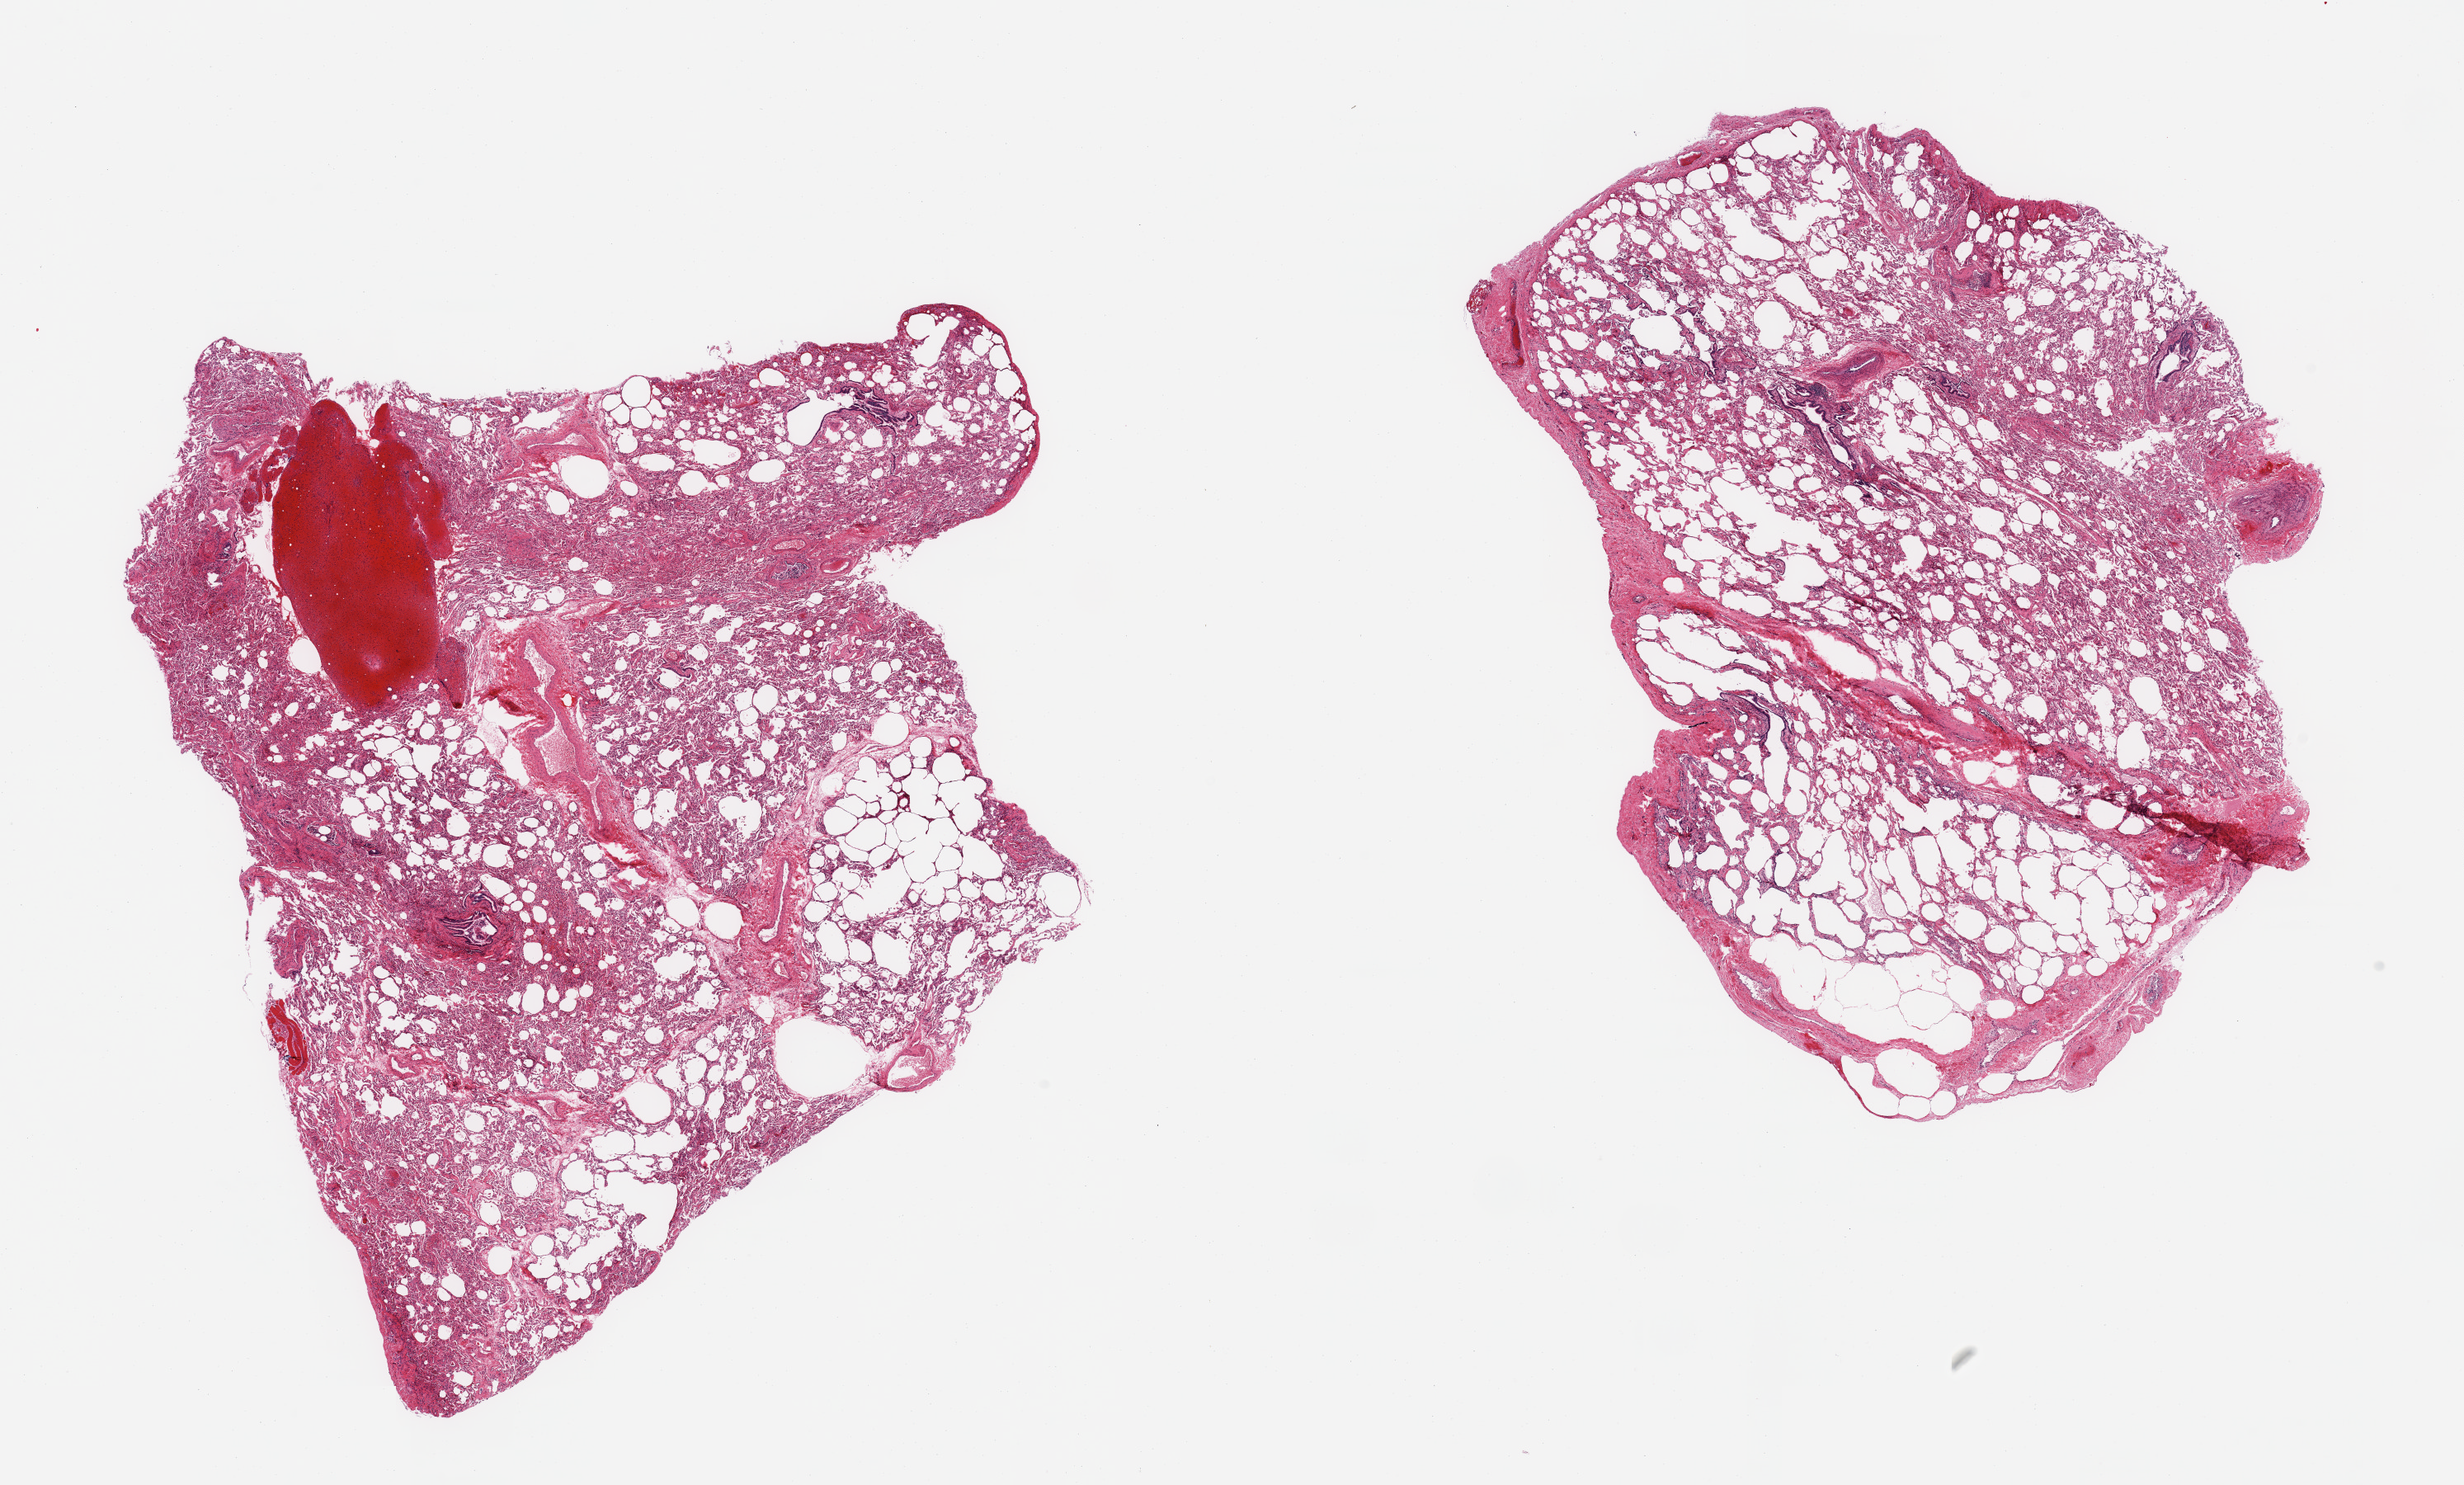
Whole-slide image, haematoxylin and eosin stain, low-resolution overview of the scanned area, about 23.6 x 14.2 mm; PAXgene-fixed paraffin-embedded (PFPE) section; section of lung (target tissue); tissue donor sample. Donor: female.
• reviewer comment on this tissue sample: 2 pieces, mild, focal edema, ataletctasis